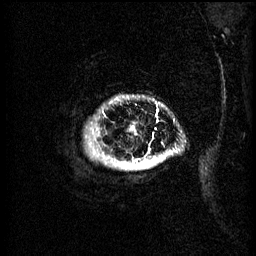
Breast MRI (dynamic contrast-enhanced), one sagittal slice; slice 59 of 60 in the series (ordered by position); 3 images stored at this slice position (order not interpretable as contrast timing); 1.5 T; TE 4.2 ms, TR 11 ms; 2 mm slice thickness; 256 × 256 image matrix. Patient: female, 51 years.
Annotated regions visible in this slice (semi-automatic segmentation, software-assisted and operator-edited):
- analysis volume of interest (the breast-tissue region the enhancement analysis was run in; not a lesion): bounding box <91,100,175,169> (left, top, right, bottom; pixels)
- tumour enhancement mask (voxels above the 70 % enhancement threshold inside the analysis volume of interest): <133,158,158,169>